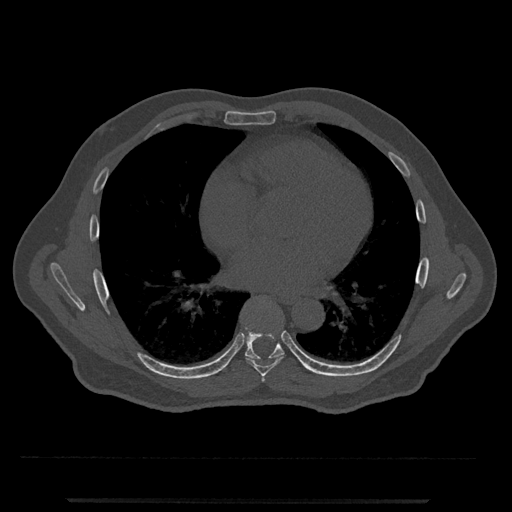
CT including the spine, one axial slice; slice 657 of 797 in the series (ordered by position); 120 kVp; bone window (W 1800 / L 400 HU); 0.5 mm slice thickness; 512 × 512 image matrix, field of view 419 × 419 mm. Male patient, age 63 years. Case-level facts recorded for this patient, not image findings: primary cancer: prostate.
Annotated regions visible in this slice (semi-automatic segmentation, software-assisted and operator-edited):
- T6 vertebra: bounding box (x1, y1, x2, y2) in pixels: (262, 376, 265, 381)
- T7 vertebra: (246, 355, 284, 377)
- T8 vertebra: (232, 311, 299, 371)